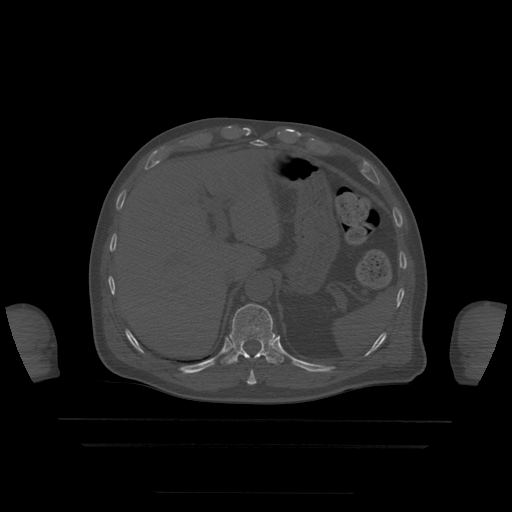
CT including the spine, one axial slice; position 225 of 522 along the scan axis; bone window (W 1800 / L 400 HU); 512 × 512 image matrix, field of view 436 × 436 mm. Patient age 68 years. From the clinical record (not read from this slice): primary cancer: urothelial.
Annotated regions visible in this slice (semi-automatically segmented with operator editing):
- T10 vertebra: bounding box <247,371,257,385> (left, top, right, bottom; pixels)
- T11 vertebra: <222,304,284,365>